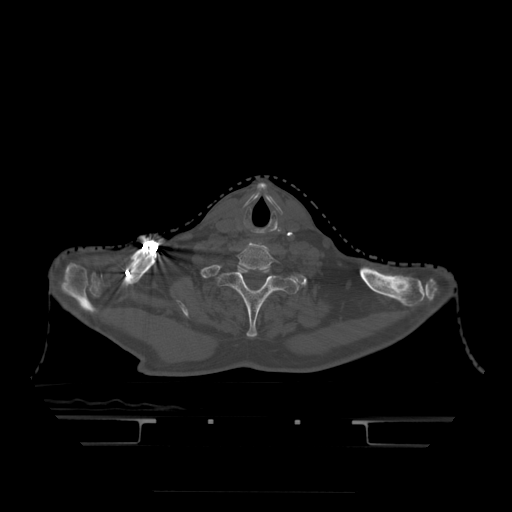
CT including the spine, one axial slice. Position 402 of 522 along the scan axis. Bone window (W 1800 / L 400 HU). 1.25 mm slice thickness. 512 × 512 image matrix, field of view 436 × 436 mm. Patient age 68 years. From the clinical record (not read from this slice): primary cancer: urothelial.
Outlined on this slice (semi-automatic segmentation, software-assisted and operator-edited):
- T1 vertebra: box from (x=220, y=265) to (x=298, y=337) px